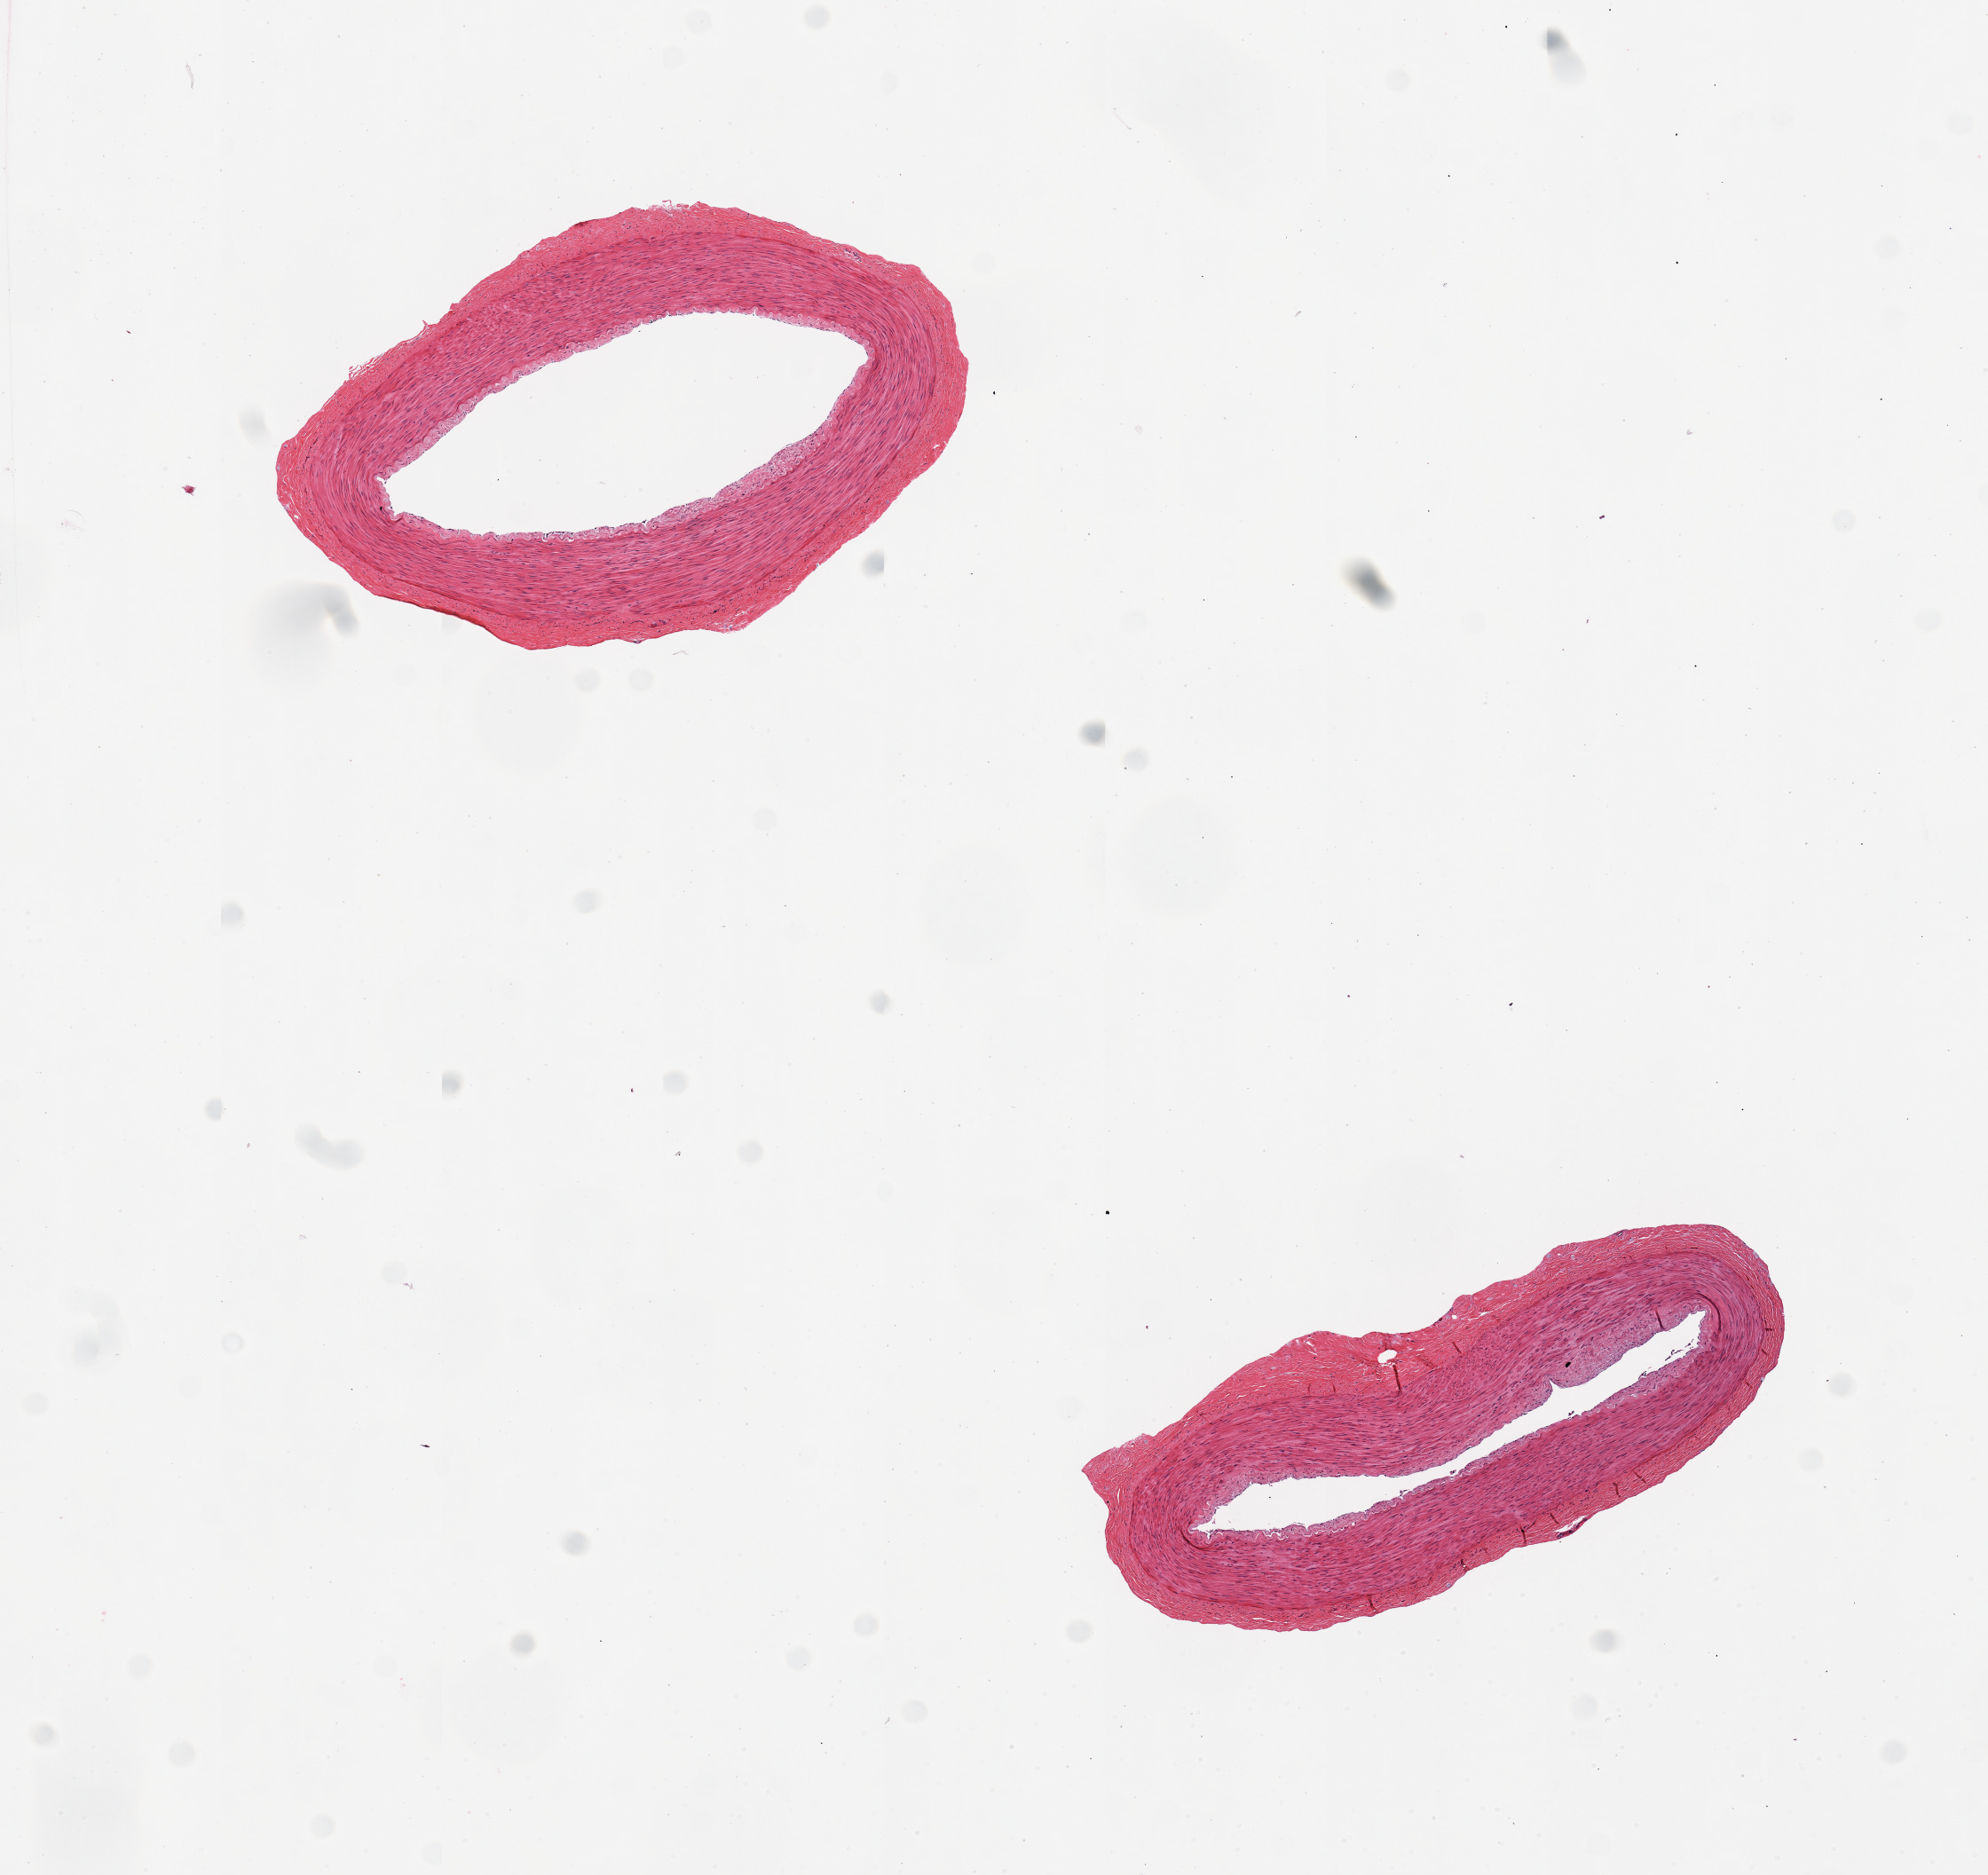
Whole-slide image, H&E stain, shown as a low-resolution overview of the whole scanned area (about 8.9 x 8.4 mm, from a 20x scan); PAXgene-fixed, paraffin-embedded tissue; target tissue: tibial artery; tissue donor sample. Donor sex: male.
Review note (as recorded): 2 pieces, well trimmed.